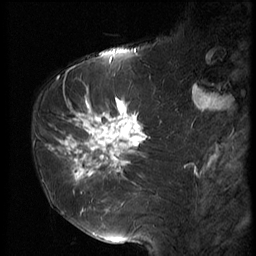
Breast MRI (dynamic contrast-enhanced), one sagittal slice. Position 25 of 56 along the scan axis. 3 images stored at this slice position (order not interpretable as contrast timing). 1.5 T. TE 4.2 ms, TR 9 ms. 2.5 mm slice thickness. 256 × 256 image matrix, field of view 180 × 180 mm. Female patient, age 61 years. Case-level facts recorded for this patient, not image findings: setting: breast cancer imaged before/during neoadjuvant chemotherapy; receptor status: HR-positive, HER2-negative.
Outlined on this slice (semi-automatically segmented with operator editing):
- analysis volume of interest (the breast-tissue region the enhancement analysis was run in; not a lesion): bounding box (x1, y1, x2, y2) in pixels: (47, 89, 153, 191)
- tumour enhancement mask (voxels above the 140 % enhancement threshold inside the analysis volume of interest): (48, 101, 148, 179)